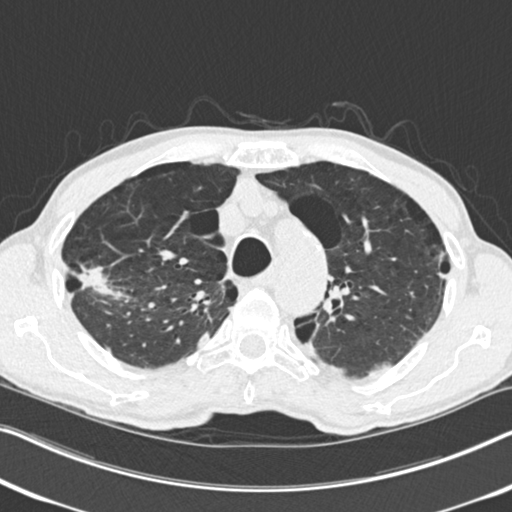
Low-dose screening chest CT, axial slice. Second annual screen. Lung window (W 1500 / L -600 HU). 2 mm slice thickness. 120 kVp. Male participant, aged 71 years at enrolment.
• Expert-annotated lung lesion, box from (x=65, y=245) to (x=137, y=318) px.
• The screening reader recorded 4 non-calcified nodules or masses ≥4 mm on this exam; which of them this box marks is not recorded.
• Later outcome: lung cancer diagnosed 83 days after this screen — adenocarcinoma, NOS, right upper lobe, well differentiated (G1), stage IA (AJCC 6th edition), 30 mm at pathology.